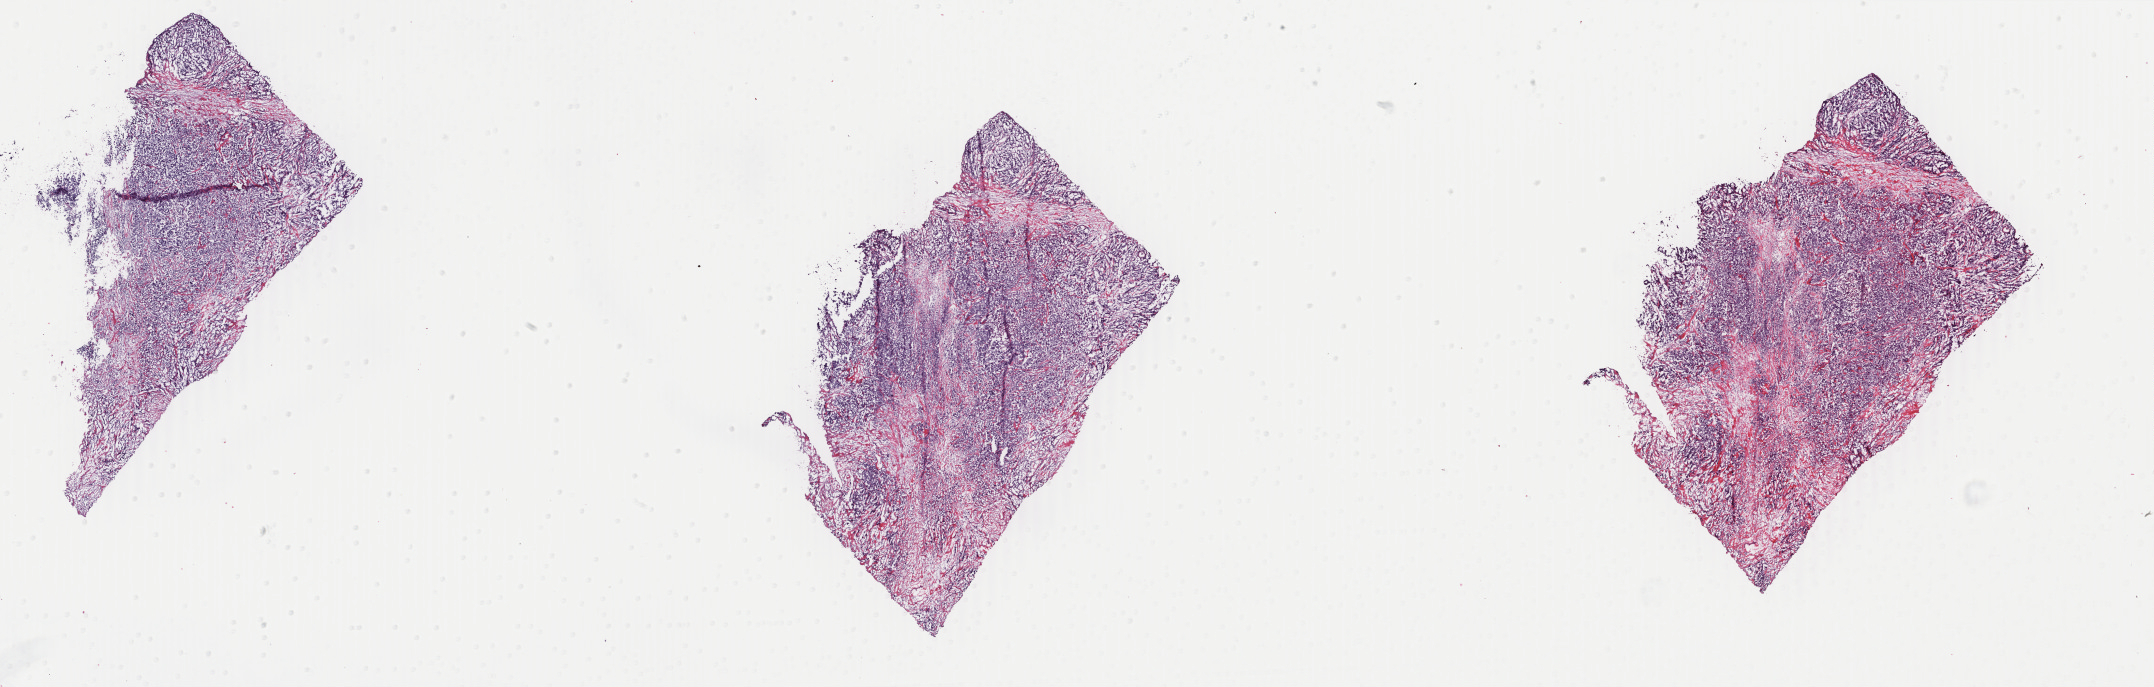
Whole-slide histology image, H&E, a low-resolution overview of the entire scanned area, about 34.3 x 10.9 mm (from a 40x scan), frozen section from the top of the tissue portion, primary tumour sample from the breast. Female patient; age at initial diagnosis 76 years. Pathologist review of this section (percent, as recorded): tumour cells 75%, tumour nuclei 75%, normal cells 0%, stromal cells 24%, necrosis 1%. Inflammatory infiltration, as recorded: lymphocyte infiltration 2%, monocyte infiltration 0%, neutrophil infiltration 0%.
• lymph nodes positive (case pathology): 0 of 2 examined
• TNM: T2 N0 (i-) M0
• pathologic diagnosis: Infiltrating duct carcinoma, NOS
• AJCC pathologic stage: IIA (6th edition)